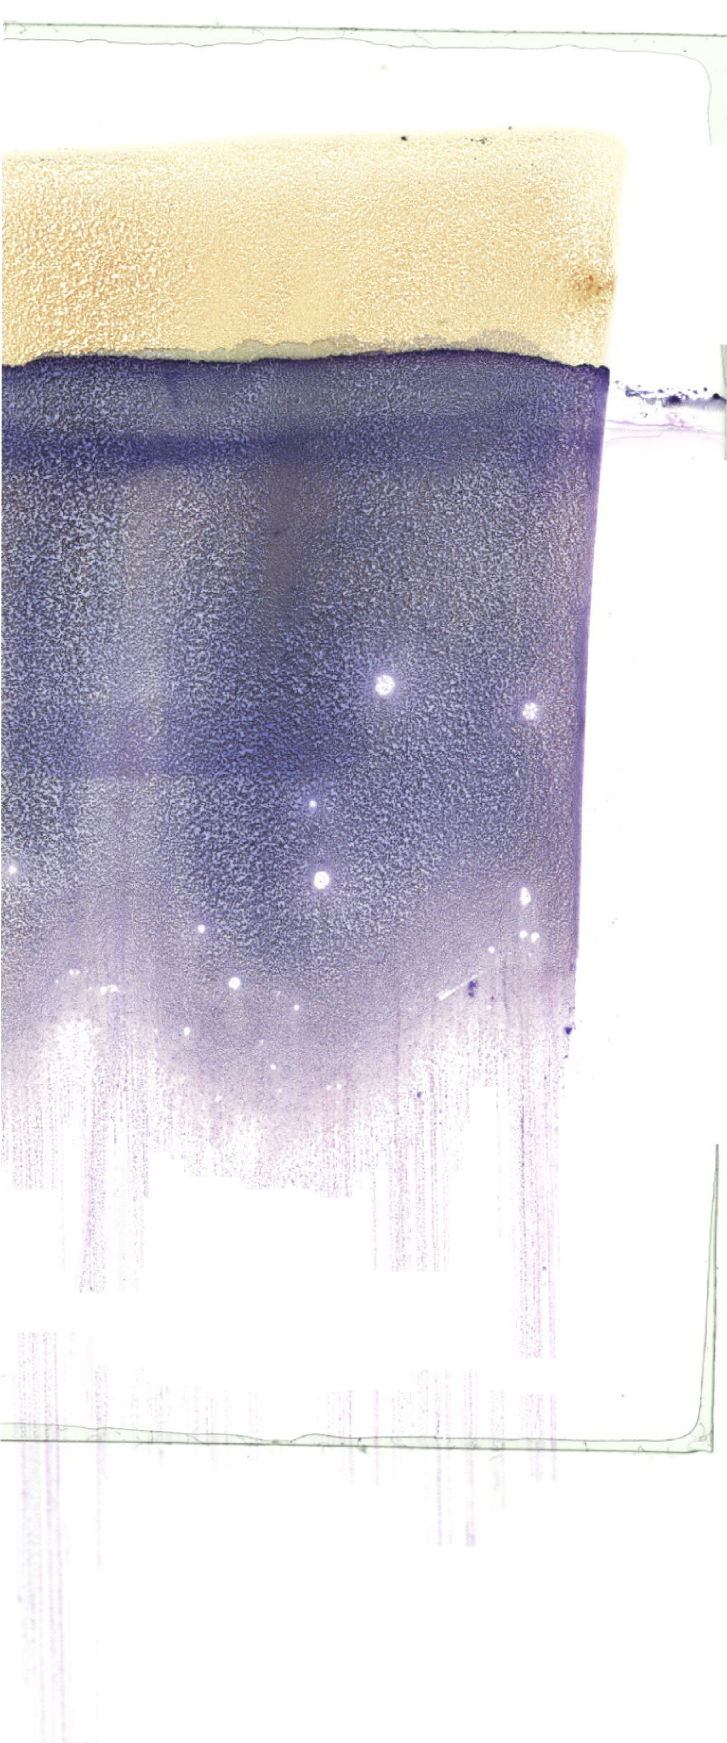
Bone marrow aspirate smear, May-Grünwald-Giemsa (MGG) stain, whole-slide image, shown as a low-resolution overview of the whole scanned area (about 20.6 x 49.4 mm). Patient sex: female.
Diagnosis: Acute Myelomonocytic Leukemia.